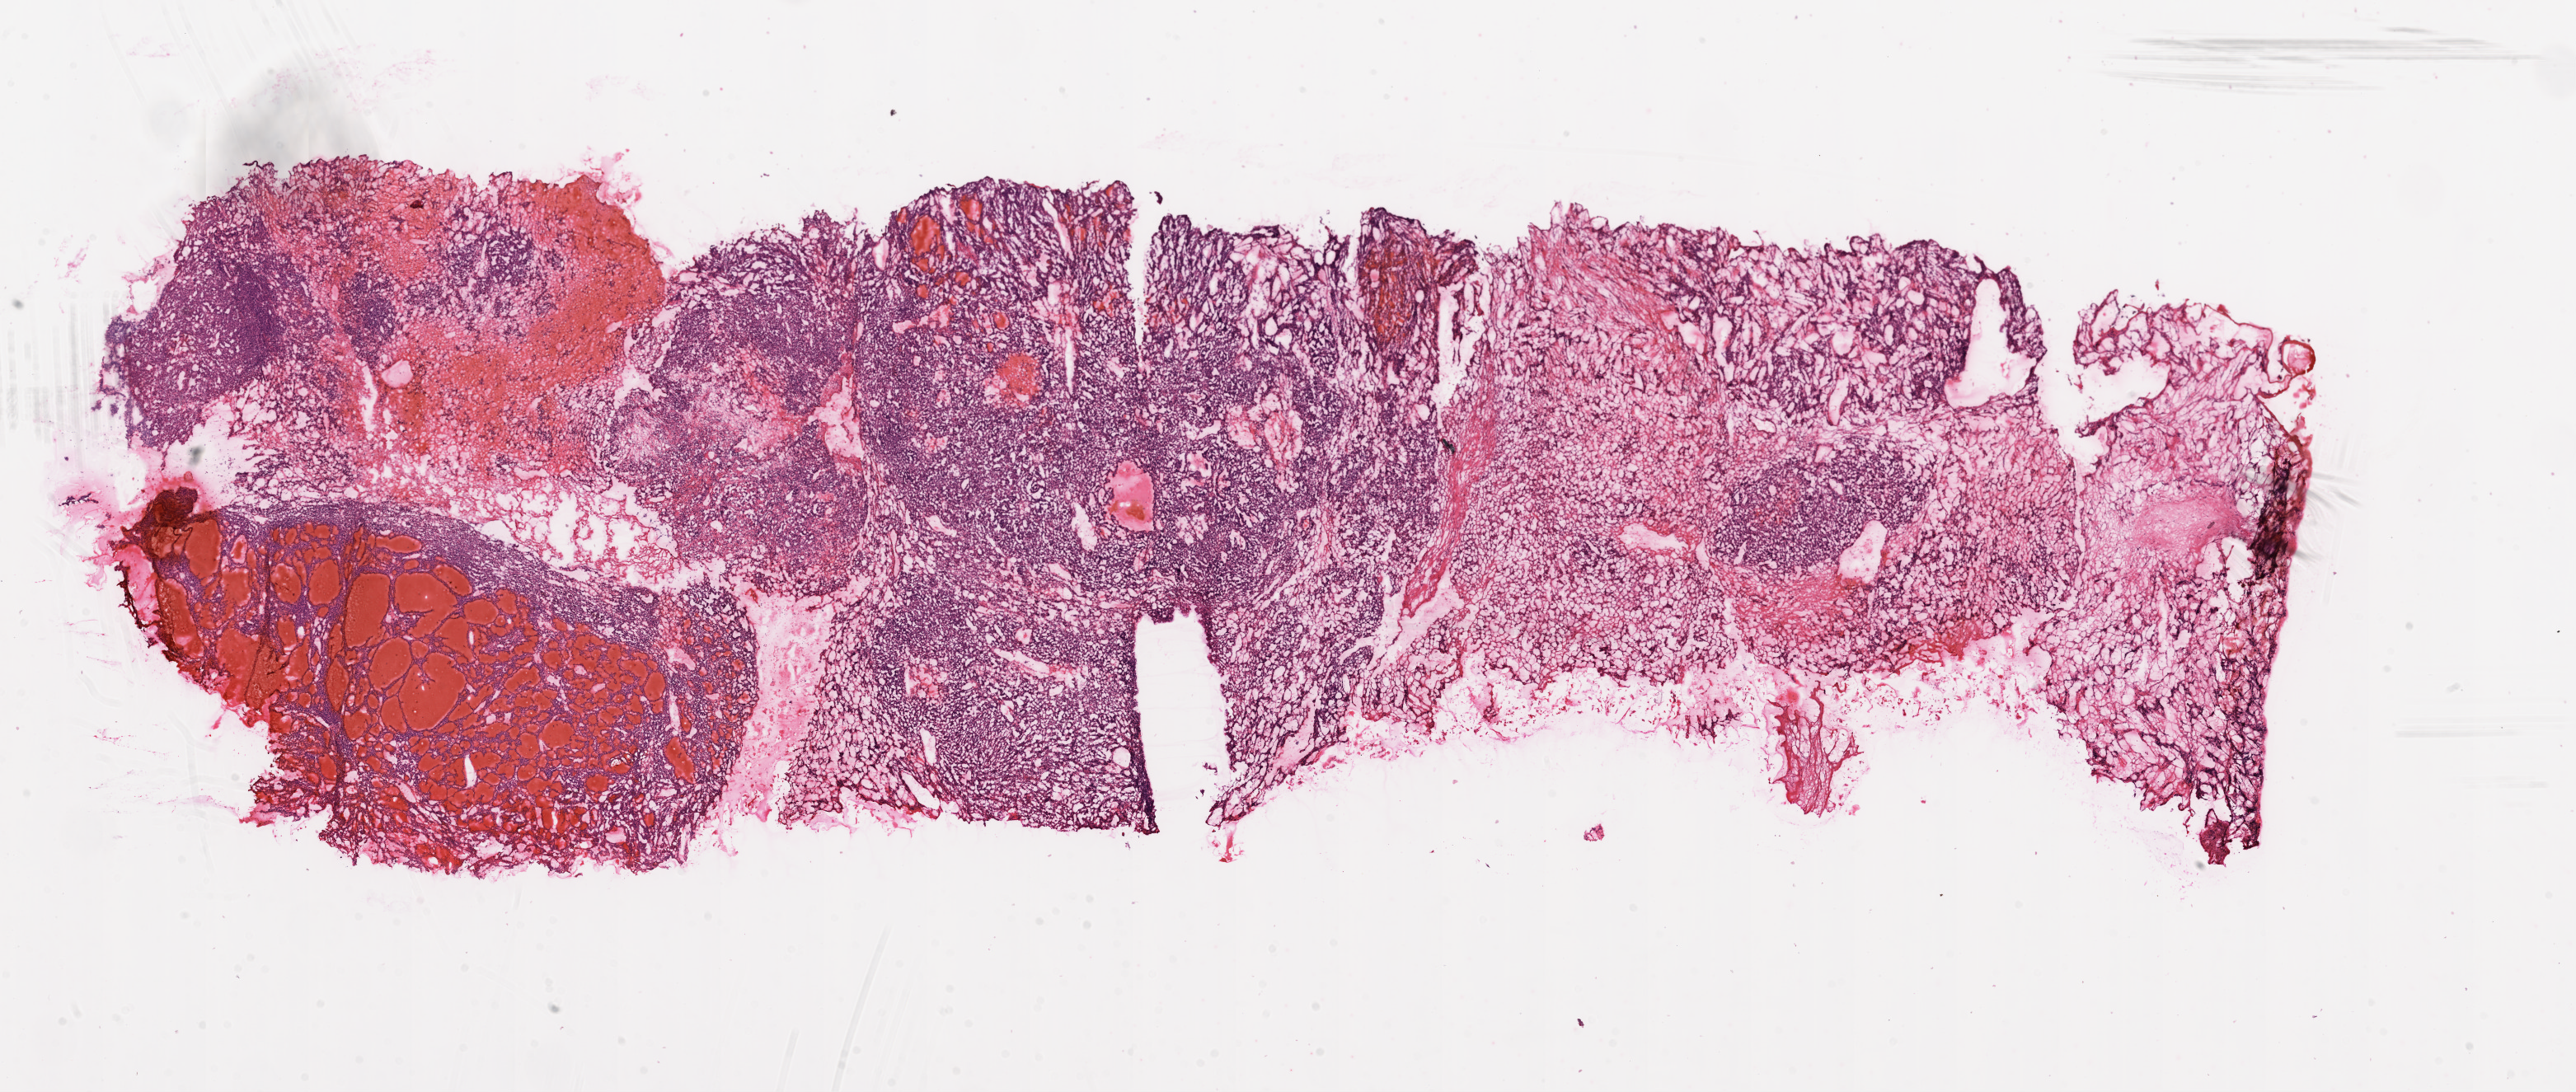
Whole-slide histology image, H&E, low-resolution overview of the scanned area, about 25.1 x 10.6 mm; frozen section from the top of the tissue portion; sample: primary tumour, kidney. Male, age 58 years at initial diagnosis. Histologic grade: G3 (poorly differentiated). Pathologist review of this section (percent, as recorded): tumour cells 90%, tumour nuclei 85%, normal cells 0%, stromal cells 10%, necrosis 0%.
AJCC pathologic stage: III. Diagnosis: Clear cell adenocarcinoma, NOS.